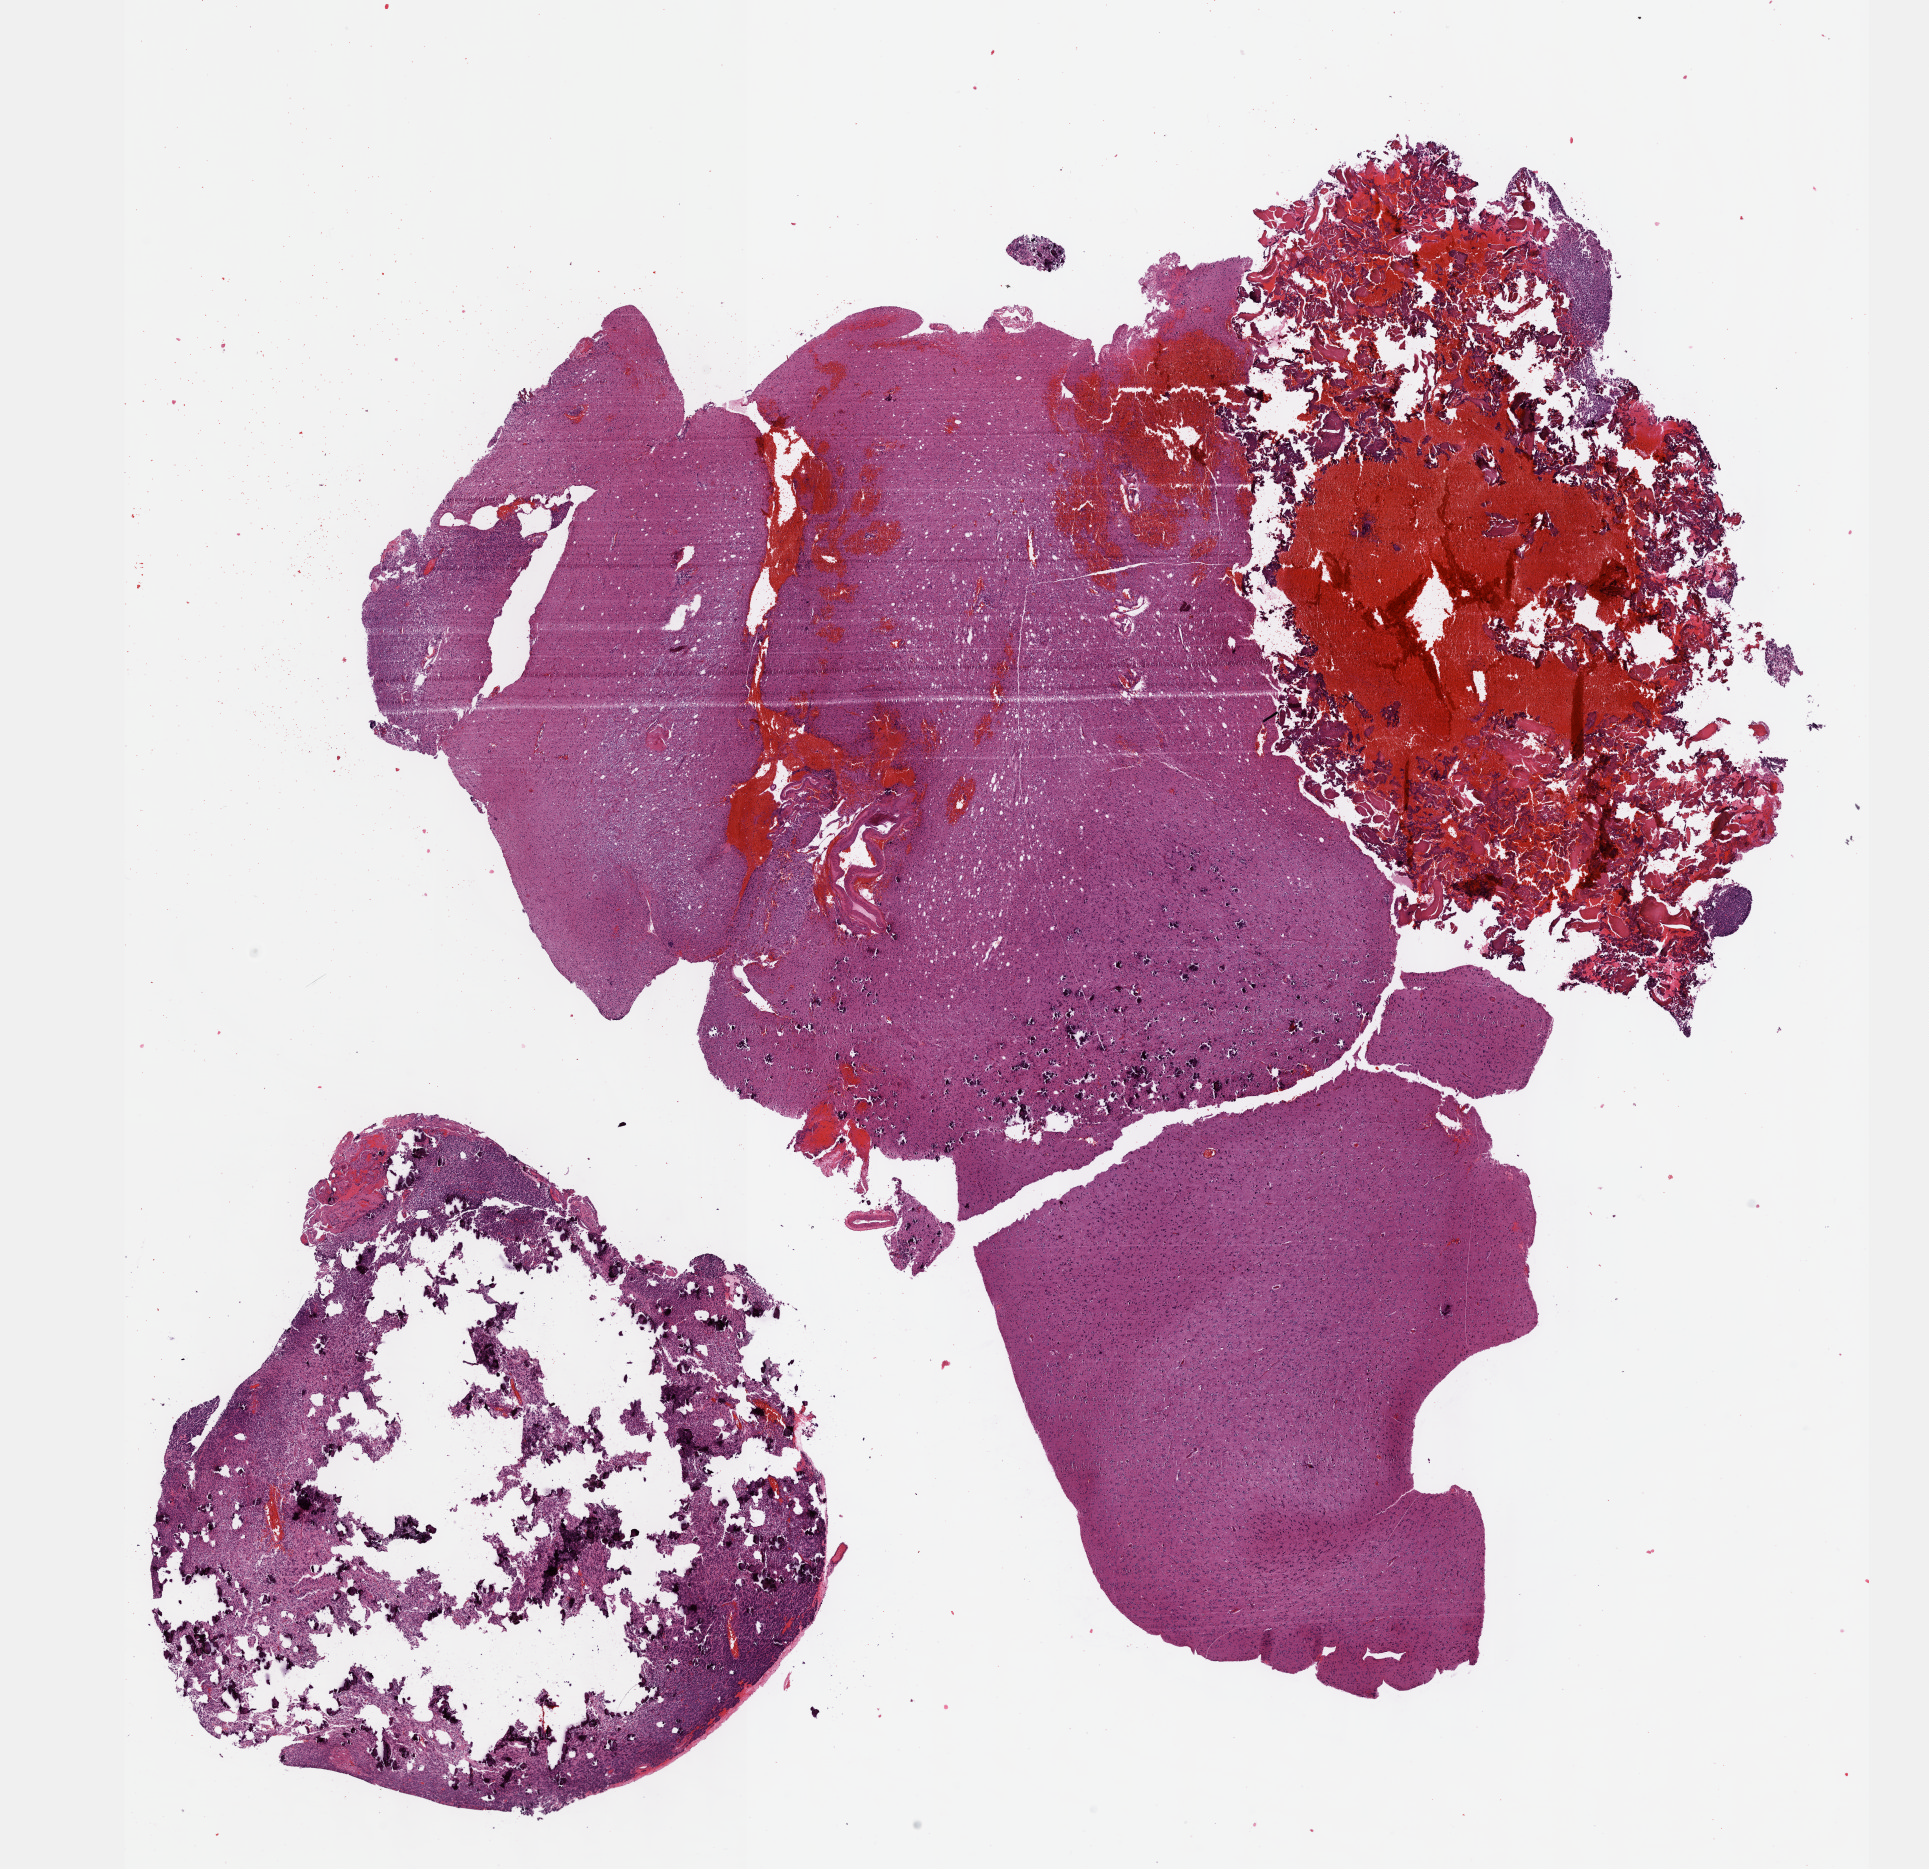
Whole-slide histology image, Hematoxylin and eosin (H&E) stained — shown as a low-resolution overview of the whole scanned area (about 15.6 x 15.1 mm); FFPE section; sample: primary tumour, brain. Patient: male, age at initial diagnosis 74 years. Histologic grade: G3 (poorly differentiated).
Diagnosis: Oligodendroglioma, anaplastic.